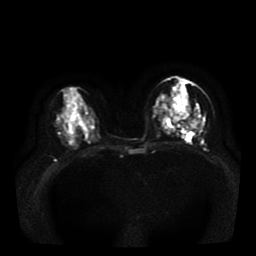
Breast MRI, one axial slice. Position 16 of 41 along the scan axis. Diffusion-weighted series; image 2 of 4 stored at this slice position (different b-values; order by instance number). 1.5 T. 256 × 256 image matrix, field of view 330 × 330 mm. Female patient.
Outlined on this slice (manually delineated by an expert):
- tumour on diffusion-weighted imaging: bounding box <174,118,180,124> (left, top, right, bottom; pixels)